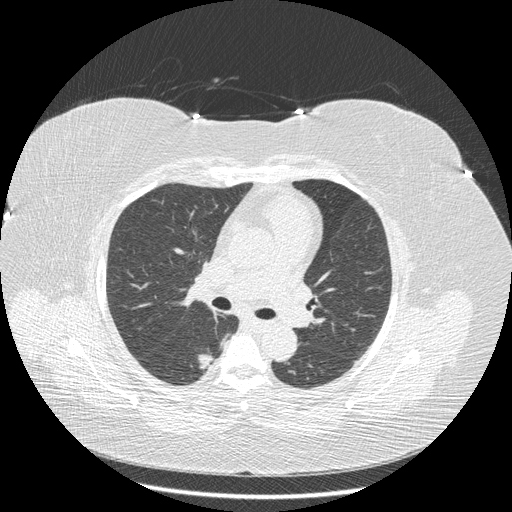
Chest CT (low-dose screening protocol), one axial image; baseline annual screen; lung window (W 1500 / L -600 HU); 1.25 mm slice thickness; standard (soft-tissue) reconstruction kernel (STANDARD); 512 × 512 image matrix, field of view 384 × 384 mm. Female, age 58 years at enrolment. Current smoker at enrolment.
- Expert-annotated lung lesion, bounding box [x1, y1, x2, y2] px = [186, 343, 227, 381].
- Screening reader's record for this exam (one nodule recorded; not confirmed to be the boxed lesion): non-calcified nodule or mass ≥4 mm, right lower lobe, 15 × 10 mm, smooth margins, soft tissue attenuation.
- Lung cancer was diagnosed 362 days after this screen: adenocarcinoma, NOS, right lower lobe, stage IB (AJCC 6th edition), 15 mm at pathology.